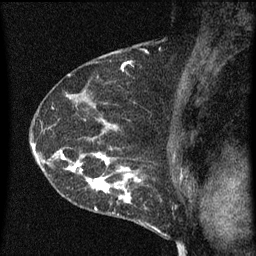
Breast MRI (dynamic contrast-enhanced), one sagittal slice. Dynamic contrast-enhanced series, image 2 of 3 at this slice position (ordered by acquisition). 1.5 T. TE 4.2 ms, TR 8 ms. 2 mm slice thickness. 256 × 256 image matrix. Patient: female, 54 years.
Annotated regions visible in this slice (semi-automatic segmentation, software-assisted and operator-edited):
- analysis volume of interest (the breast-tissue region the enhancement analysis was run in; not a lesion): bounding box (x1, y1, x2, y2) in pixels: (49, 138, 164, 209)
- tumour enhancement mask (voxels above the 70 % enhancement threshold inside the analysis volume of interest): (50, 148, 163, 209)